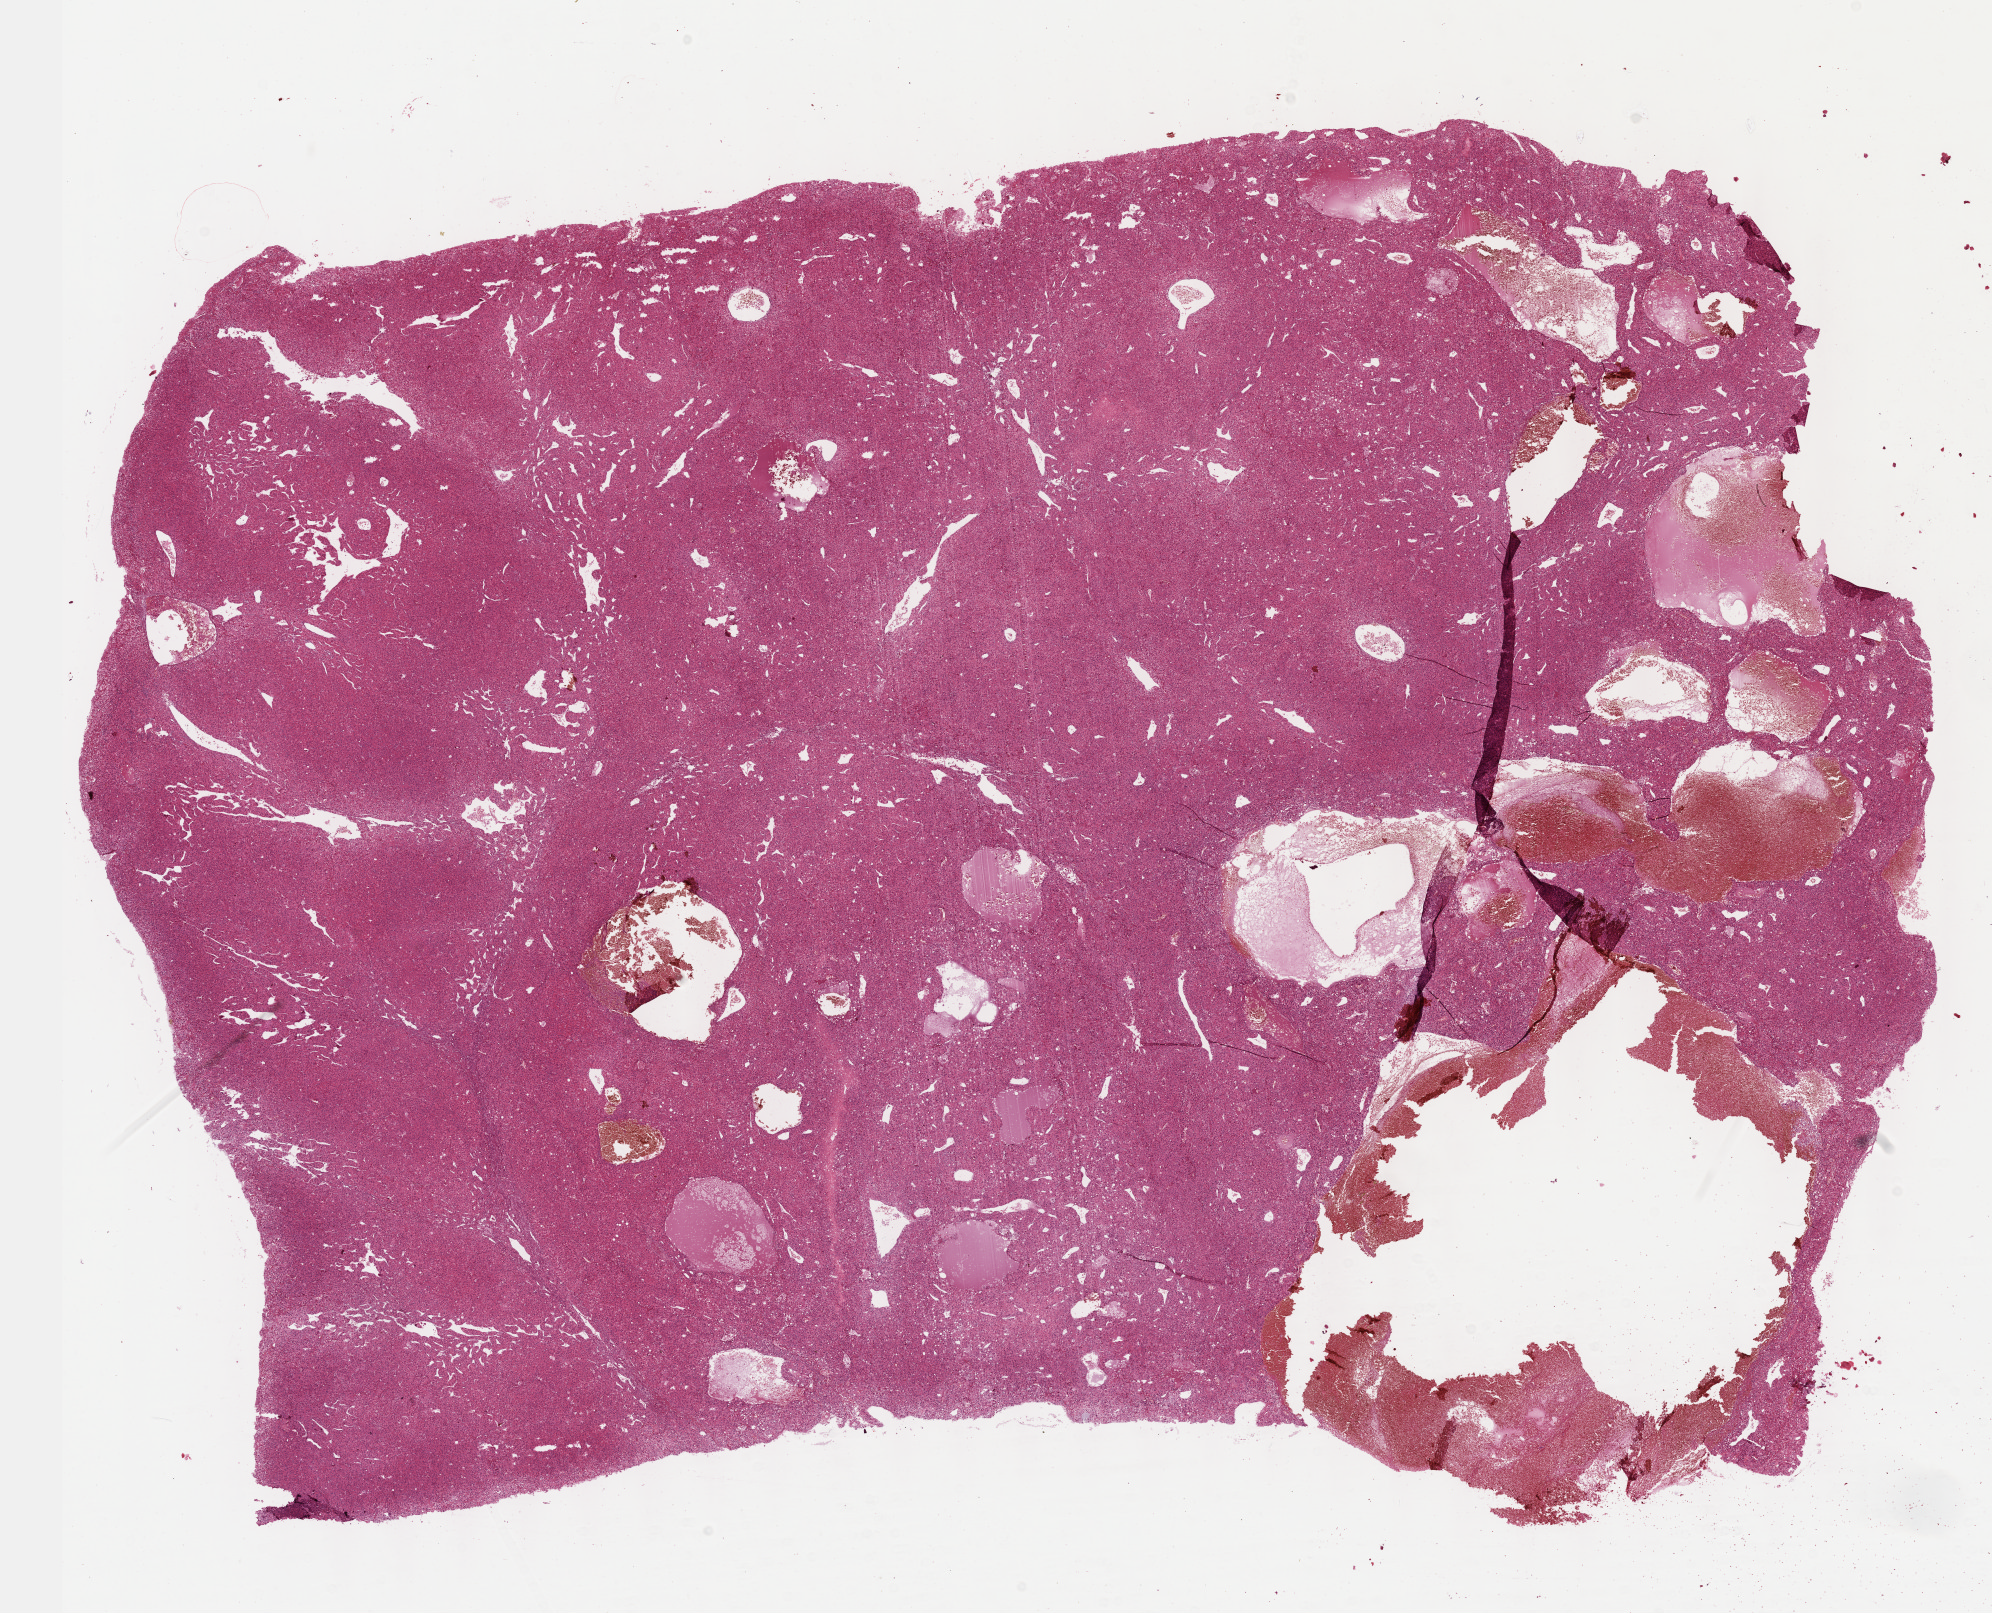
Hematoxylin and eosin (H&E) stained whole-slide image, low-resolution overview of the scanned area, about 16.1 x 13.0 mm (slide scanned at 40x), FFPE section, primary tumour sample from the liver. Male, age 61 years at initial diagnosis.
Diagnosis: Hepatocellular carcinoma, NOS.